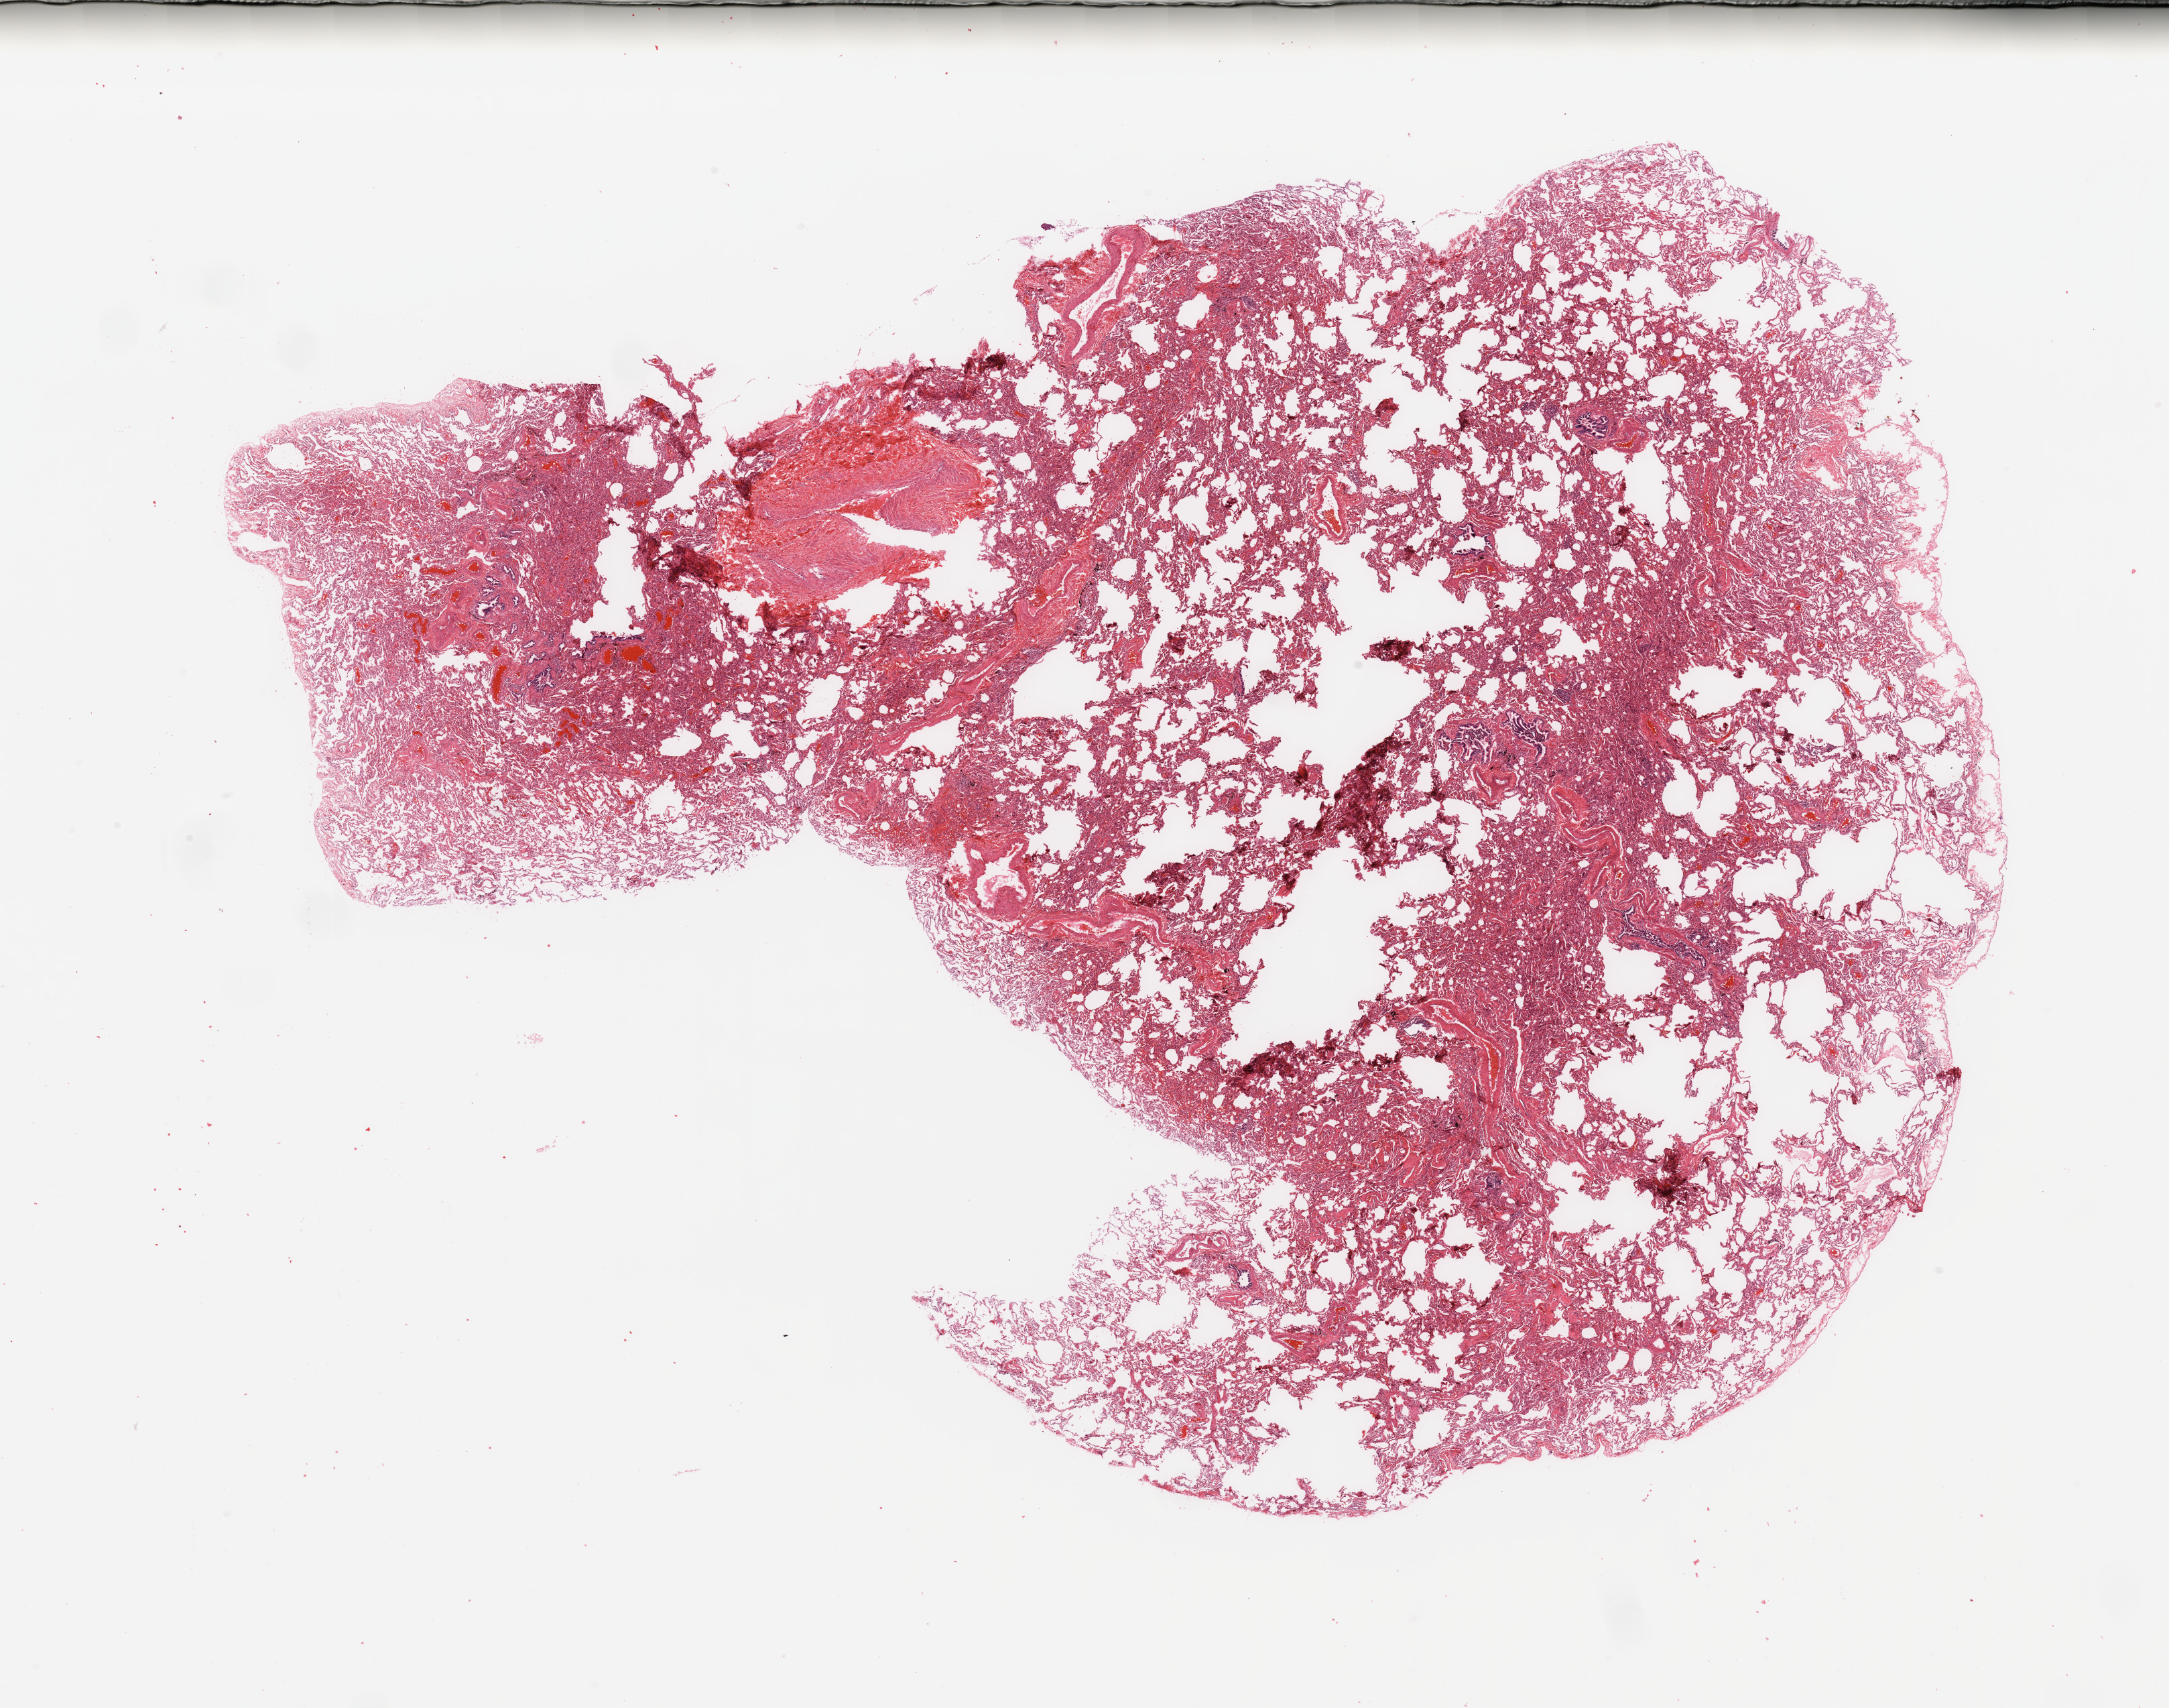
Hematoxylin and eosin (H&E) stained whole-slide image, low-resolution overview of the scanned area, about 25.6 x 20.2 mm (acquisition: 20x scan). Lung, normal (non-tumour) tissue. 72-year-old female patient.
• this section: normal (non-tumour) tissue from the same patient
• patient diagnosis: Adenocarcinoma, NOS